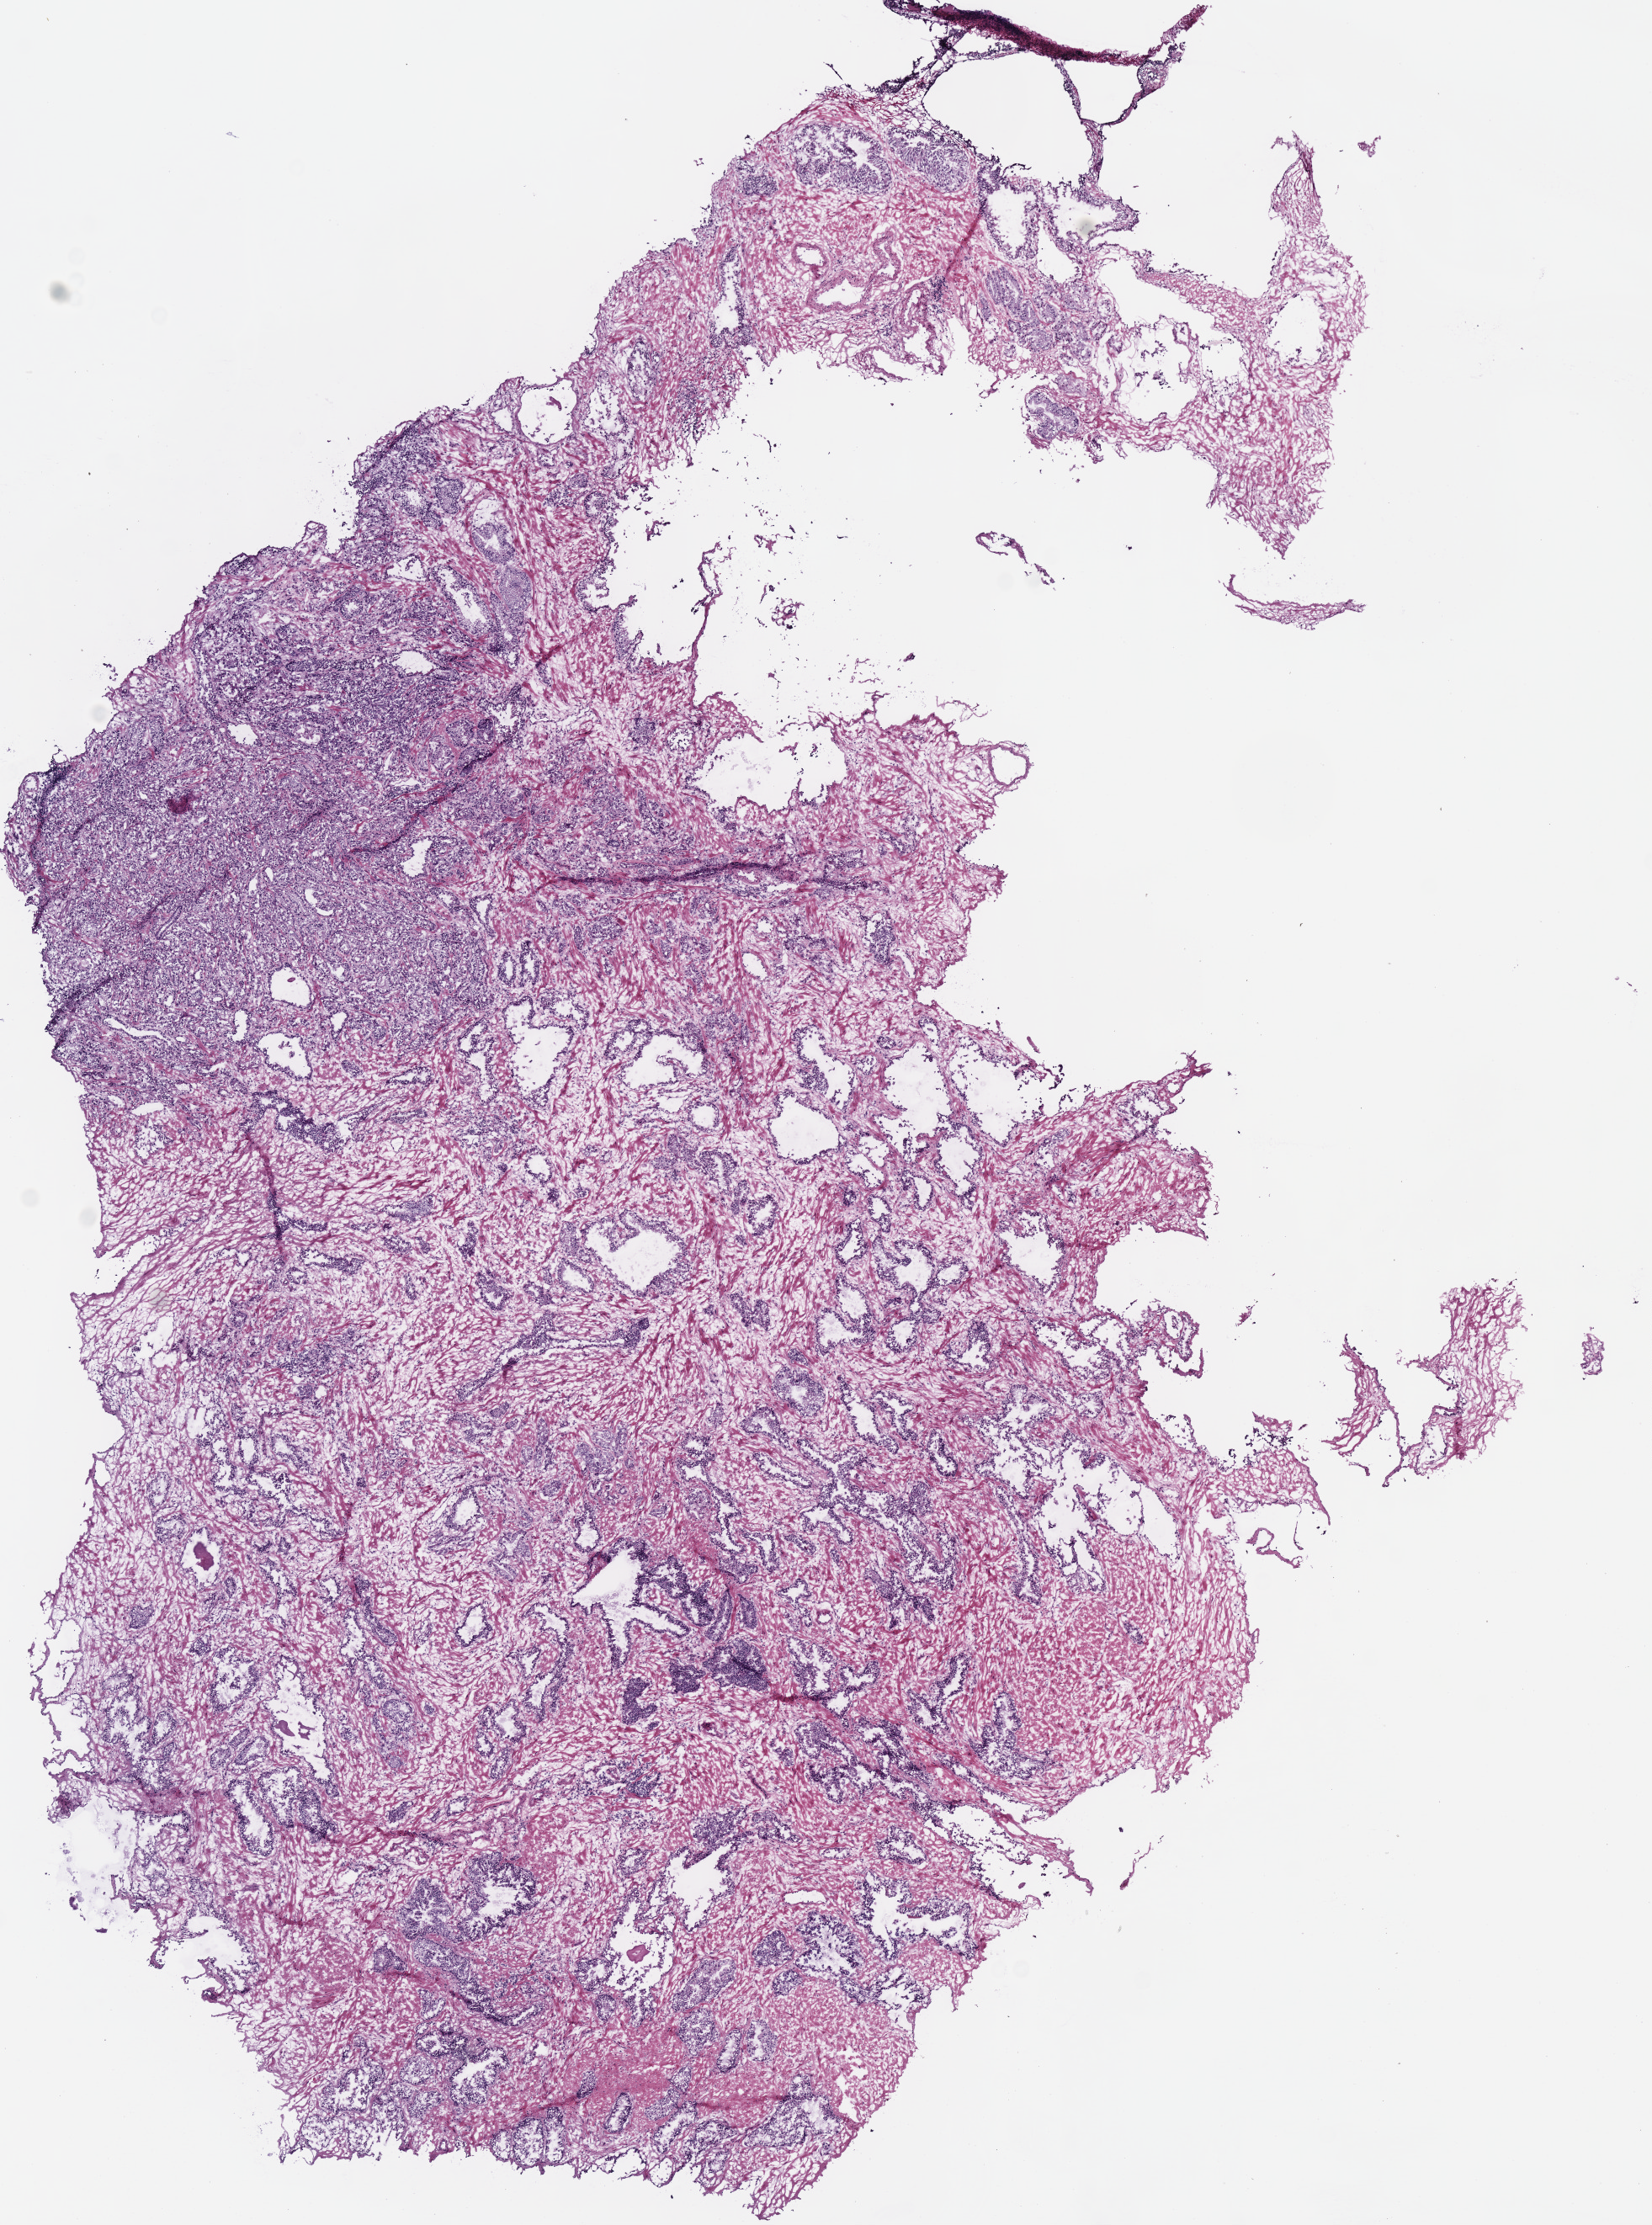
Hematoxylin and eosin (H&E) stained whole-slide image, low-resolution overview of the scanned area, about 7.7 x 10.4 mm (acquisition: 40x scan). Frozen section from the top of the tissue portion. Solid tissue normal (non-tumour tissue) sample from the prostate. Male, age 65 years at initial diagnosis.
- this section: solid tissue normal (non-tumour) sample from the same patient
- patient diagnosis: Acinar cell carcinoma (prostate gland)